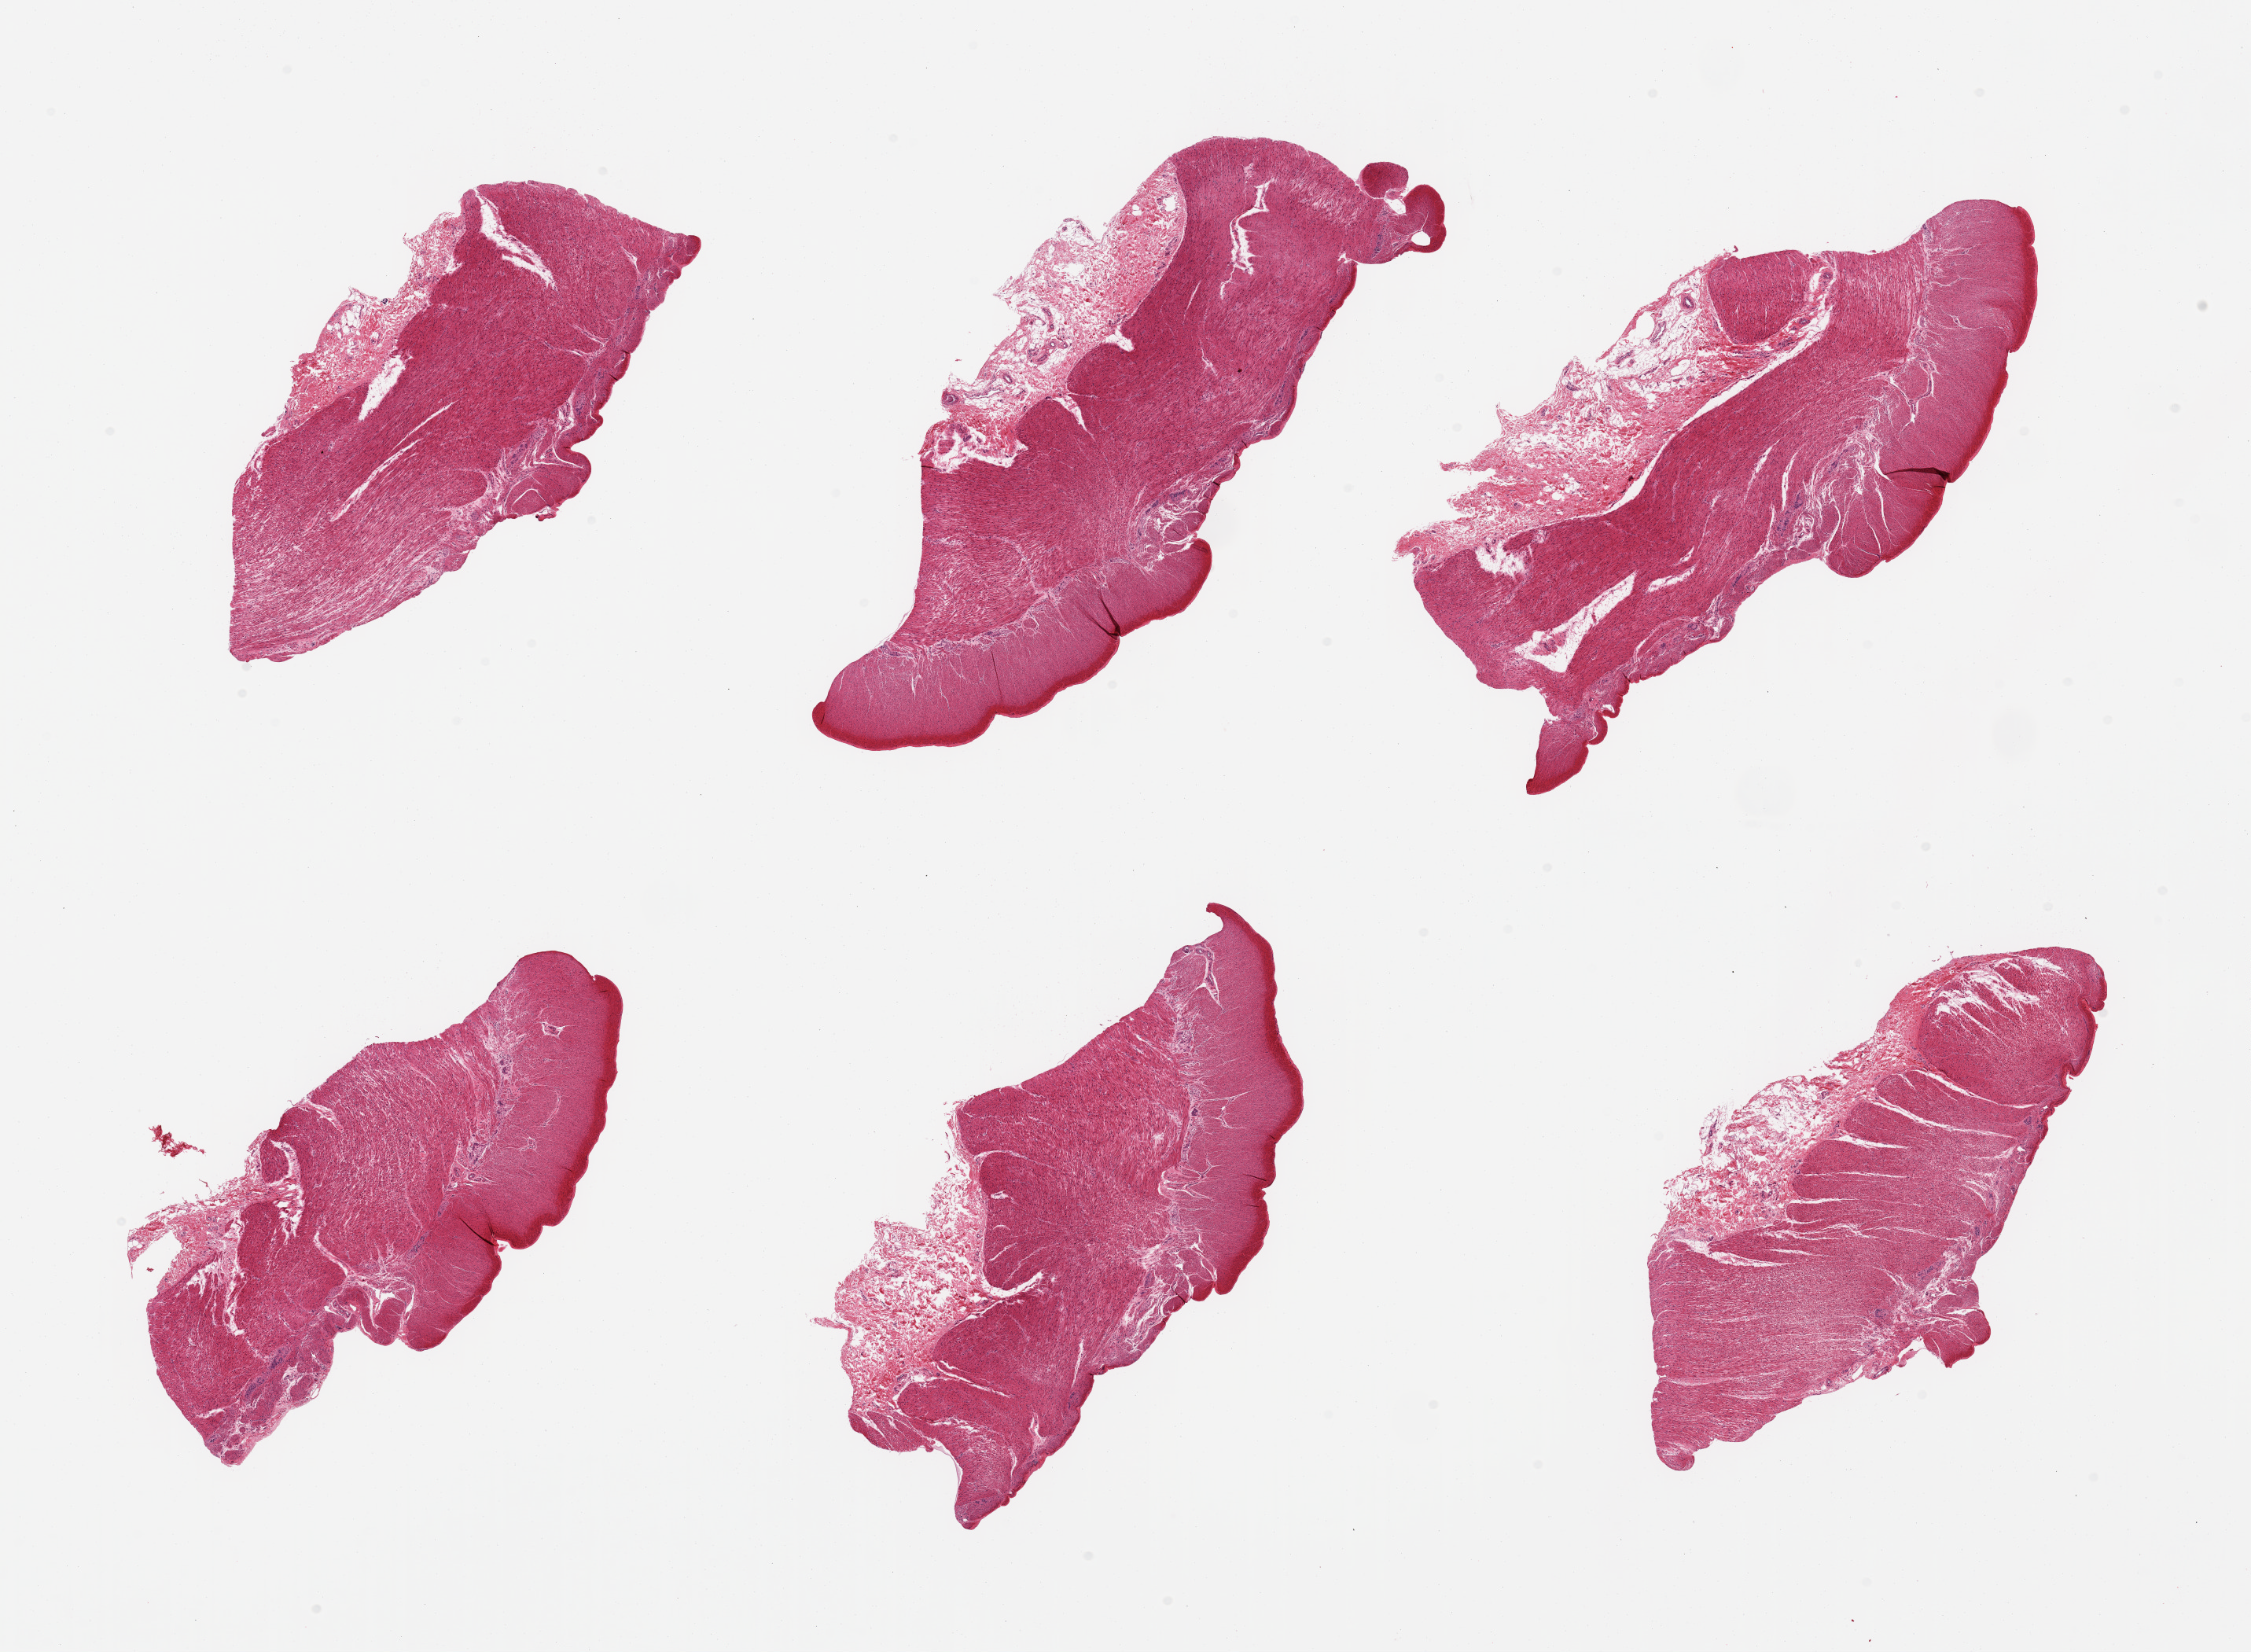
Haematoxylin and eosin whole-slide image — shown as a low-resolution overview of the whole scanned area (about 22.6 x 16.6 mm). PAXgene-fixed, paraffin-embedded tissue. Section of sigmoid colon (target tissue). Donor tissue sample. Donor sex: female.
Pathologist's review note for this sample: 6 pieces; confirmed target muscularis, trace adherent serosal fibrous tissue.